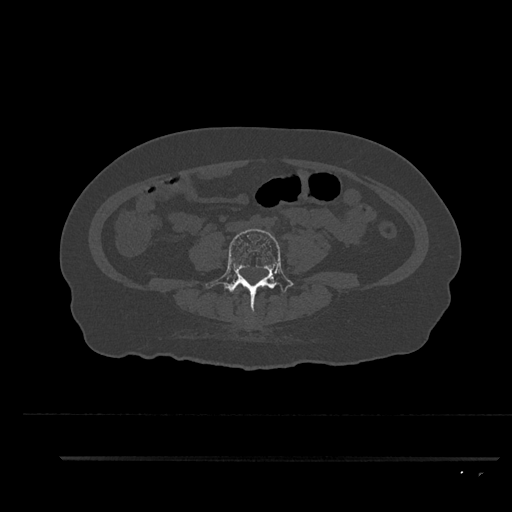
CT including the spine, one axial slice; position 27 of 797 along the scan axis; bone window (W 1800 / L 400 HU); 512 × 512 image matrix, field of view 408 × 408 mm. Female patient, age 44 years. From the clinical record (not read from this slice): primary cancer: renal; vertebrae with lytic lesions (as recorded): L1.
Outlined on this slice (semi-automatically segmented with operator editing):
- L4 vertebra: bounding box [x1, y1, x2, y2] px = [206, 229, 294, 312]